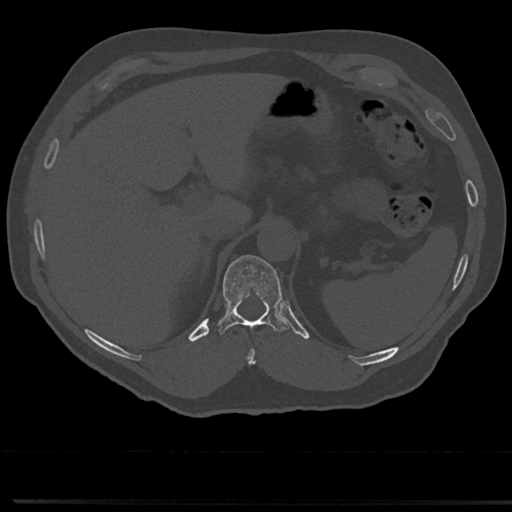
CT including the spine, one axial slice; position 209 of 817 along the scan axis; reconstruction kernel Br40s/3; 120 kVp; bone window (W 1800 / L 400 HU); 512 × 512 image matrix. Male patient, age 61 years. Case-level facts recorded for this patient, not image findings: primary cancer: prostate.
Outlined on this slice (semi-automatically segmented with operator editing):
- T10 vertebra: bounding box [x1, y1, x2, y2] px = [246, 336, 256, 366]
- T11 vertebra: [214, 256, 289, 336]